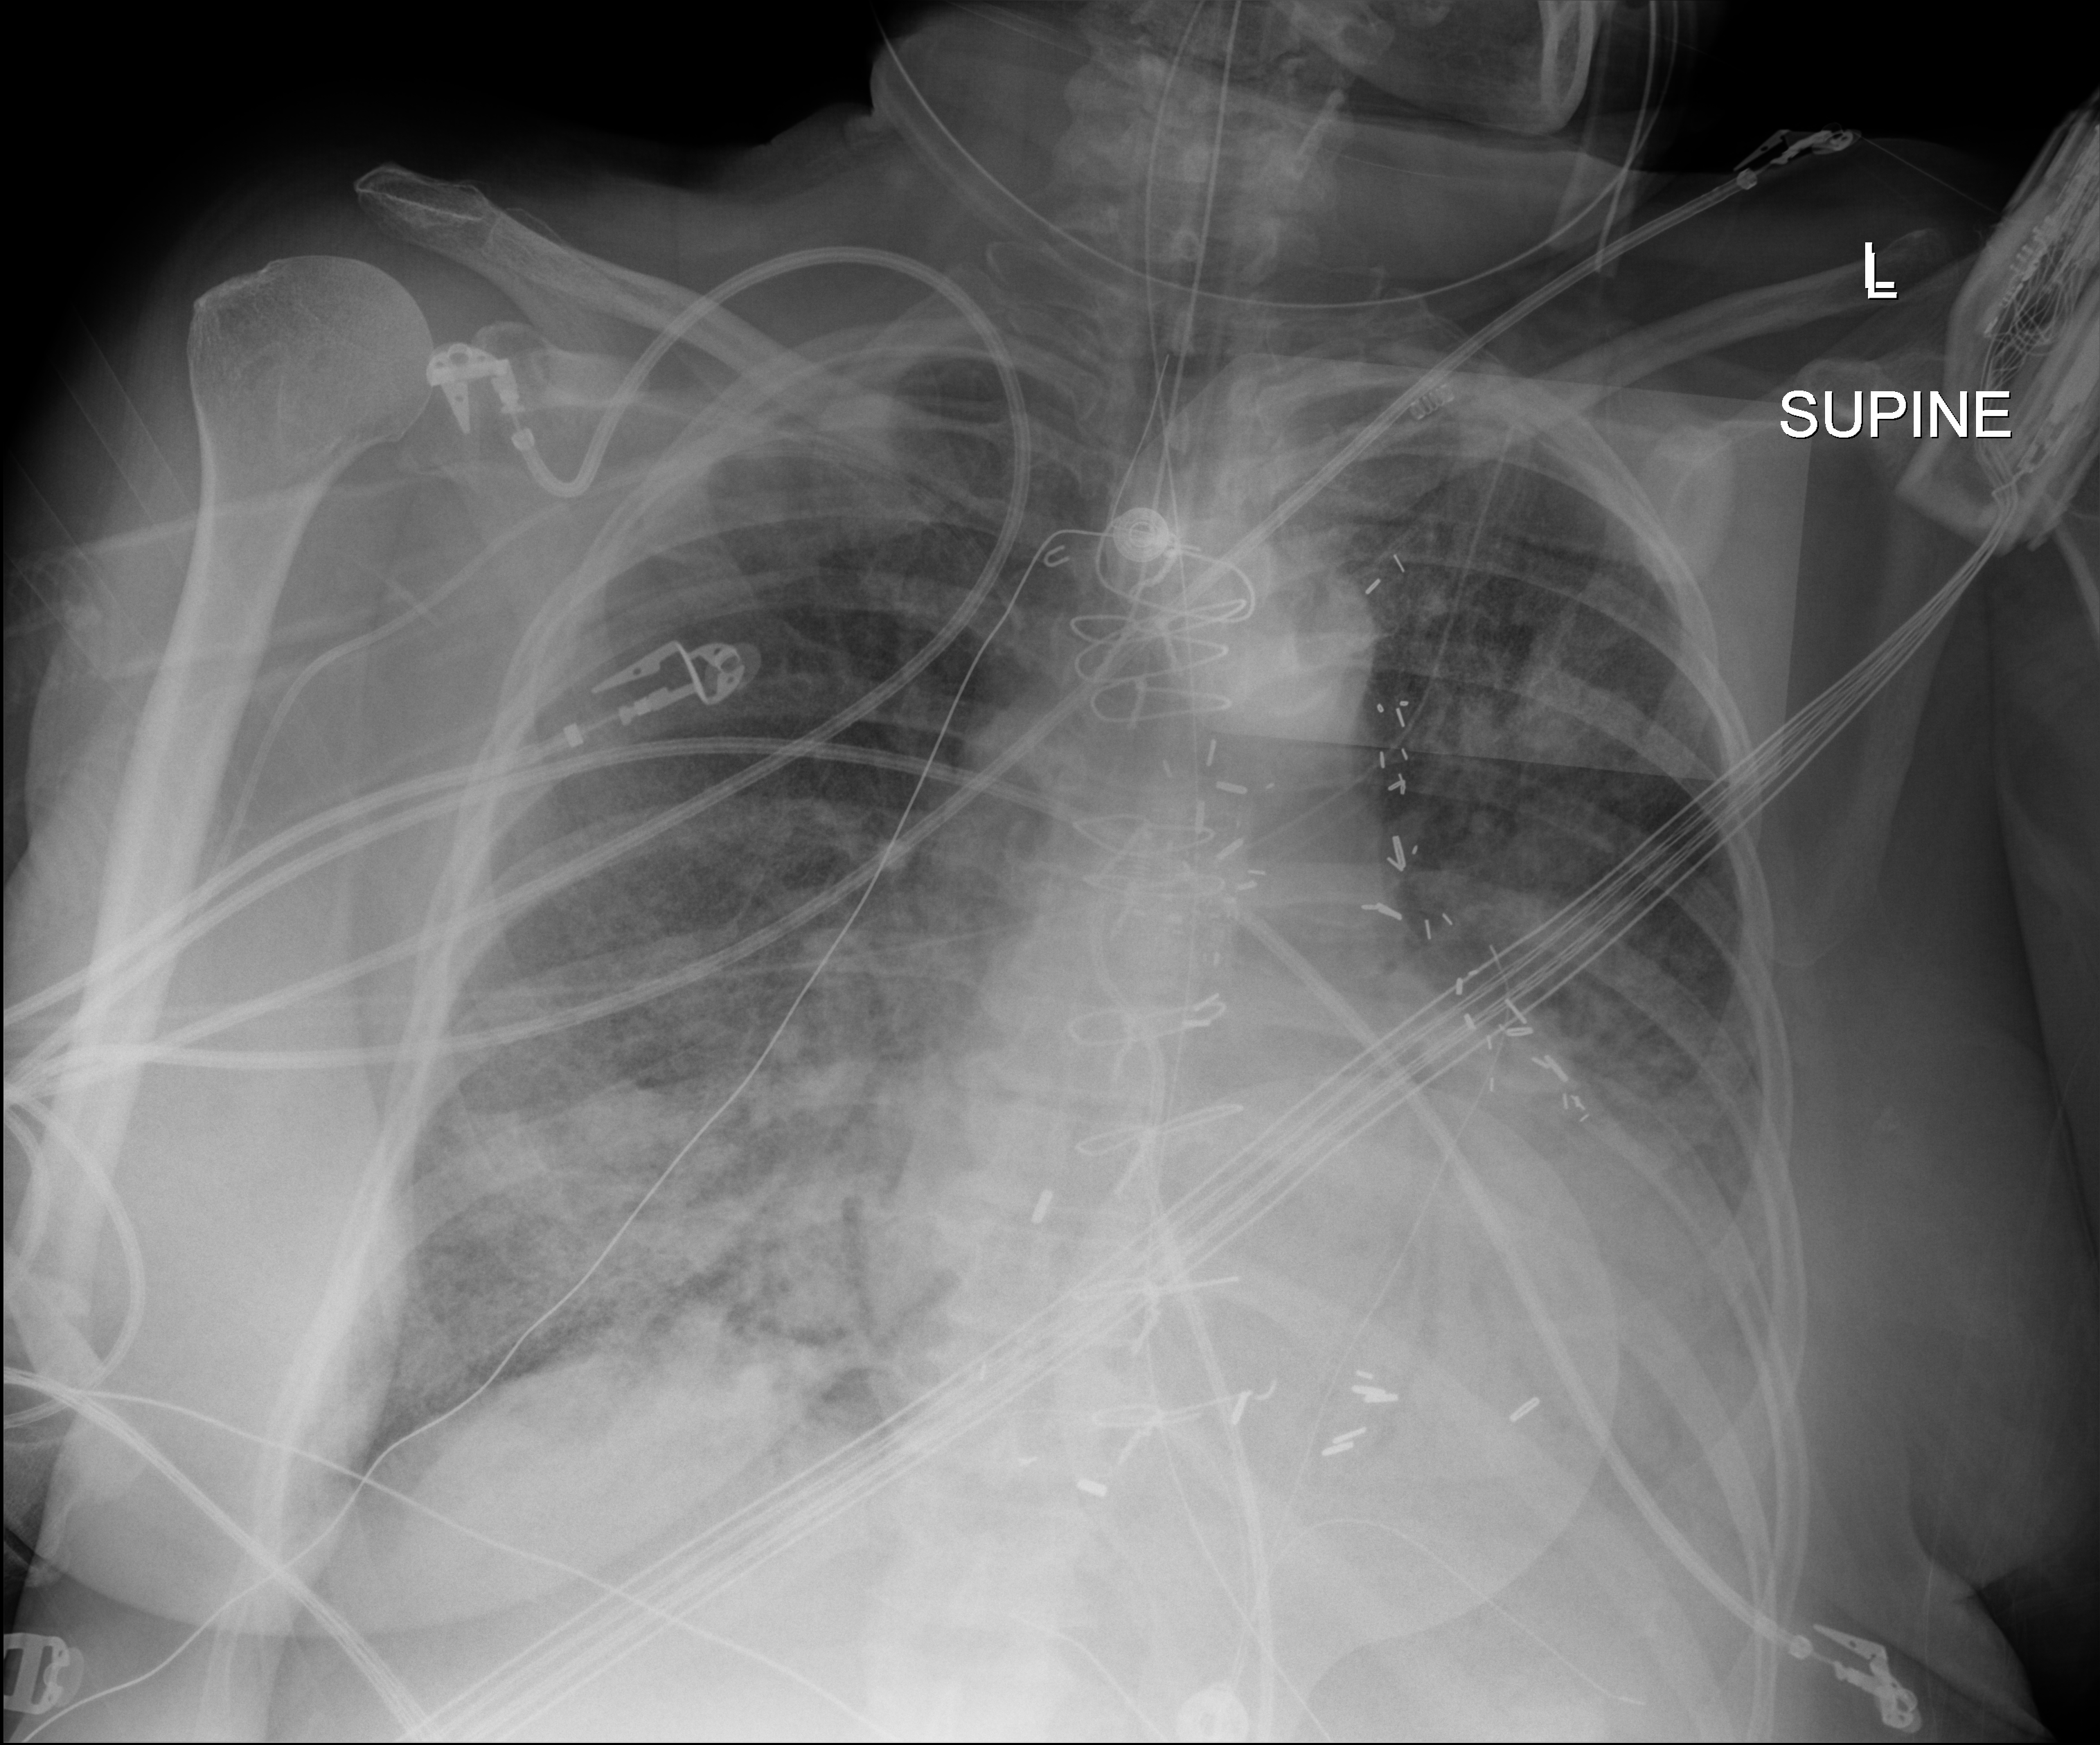
Portable chest radiograph, anteroposterior (AP) projection. Female patient hospitalised with COVID-19, age 60–74 years.
From the hospital-stay record, not from the radiograph (when in the stay this image was taken is not recorded): length of hospital stay: 25 days.